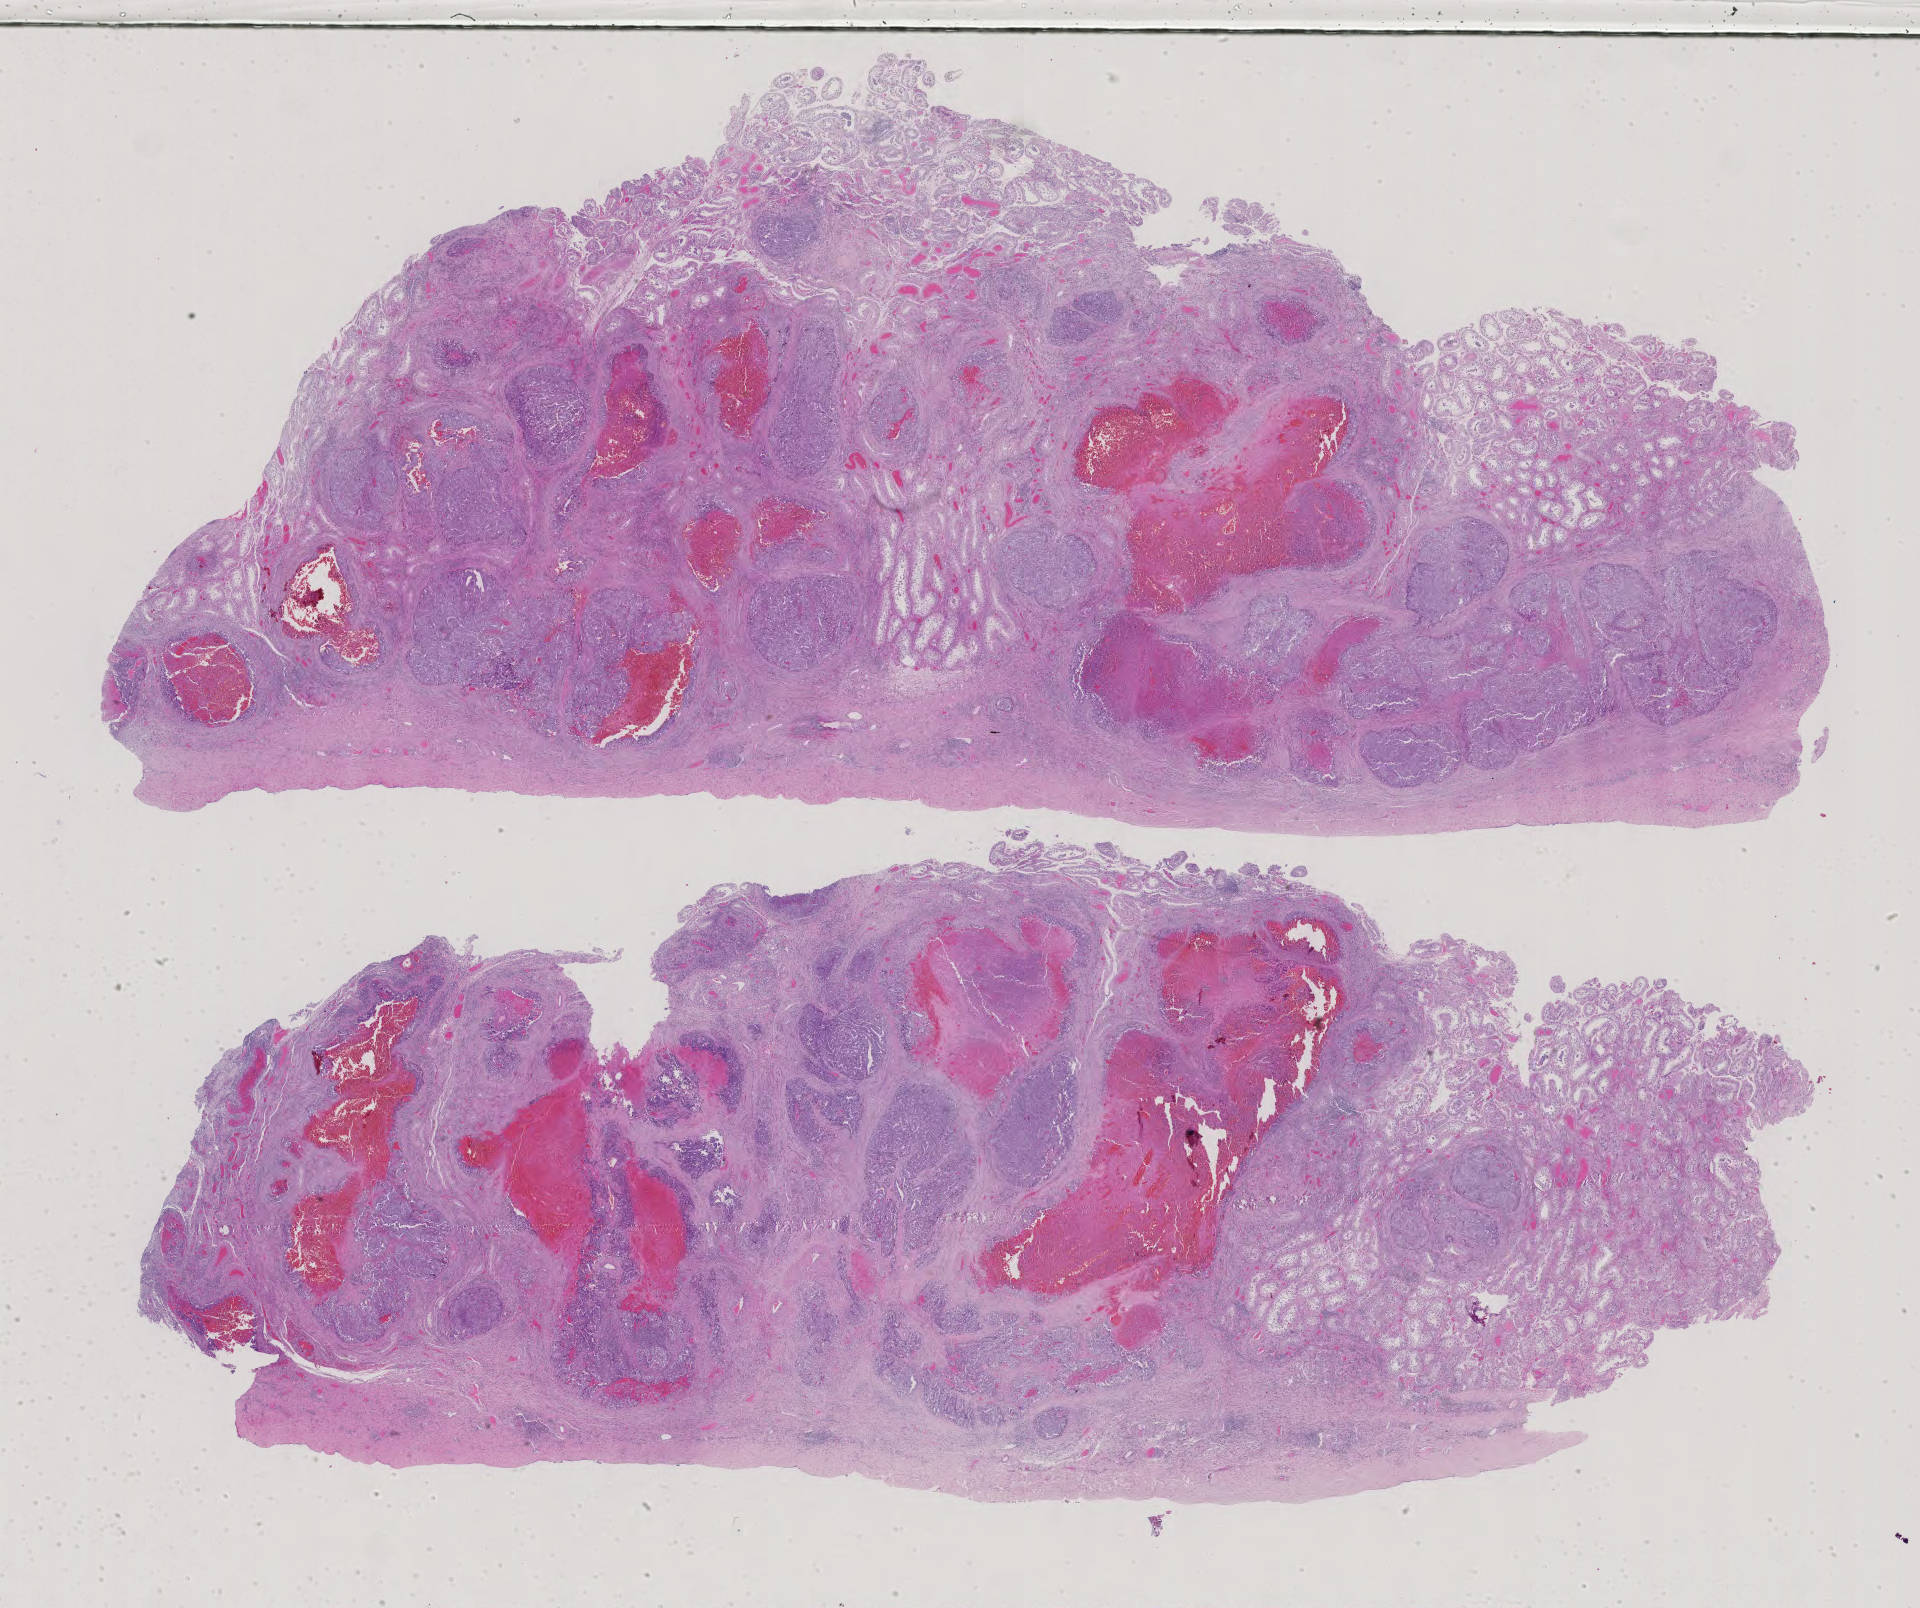
Digitized Hematoxylin and eosin (H&E) stained tissue section (whole slide) — whole scanned area (about 28.0 x 23.4 mm) shown as a low-resolution overview, formalin-fixed paraffin-embedded (FFPE) diagnostic section, sample: primary tumour, testis. Male, age 35 years at initial diagnosis.
Diagnosis: Embryonal carcinoma, NOS.